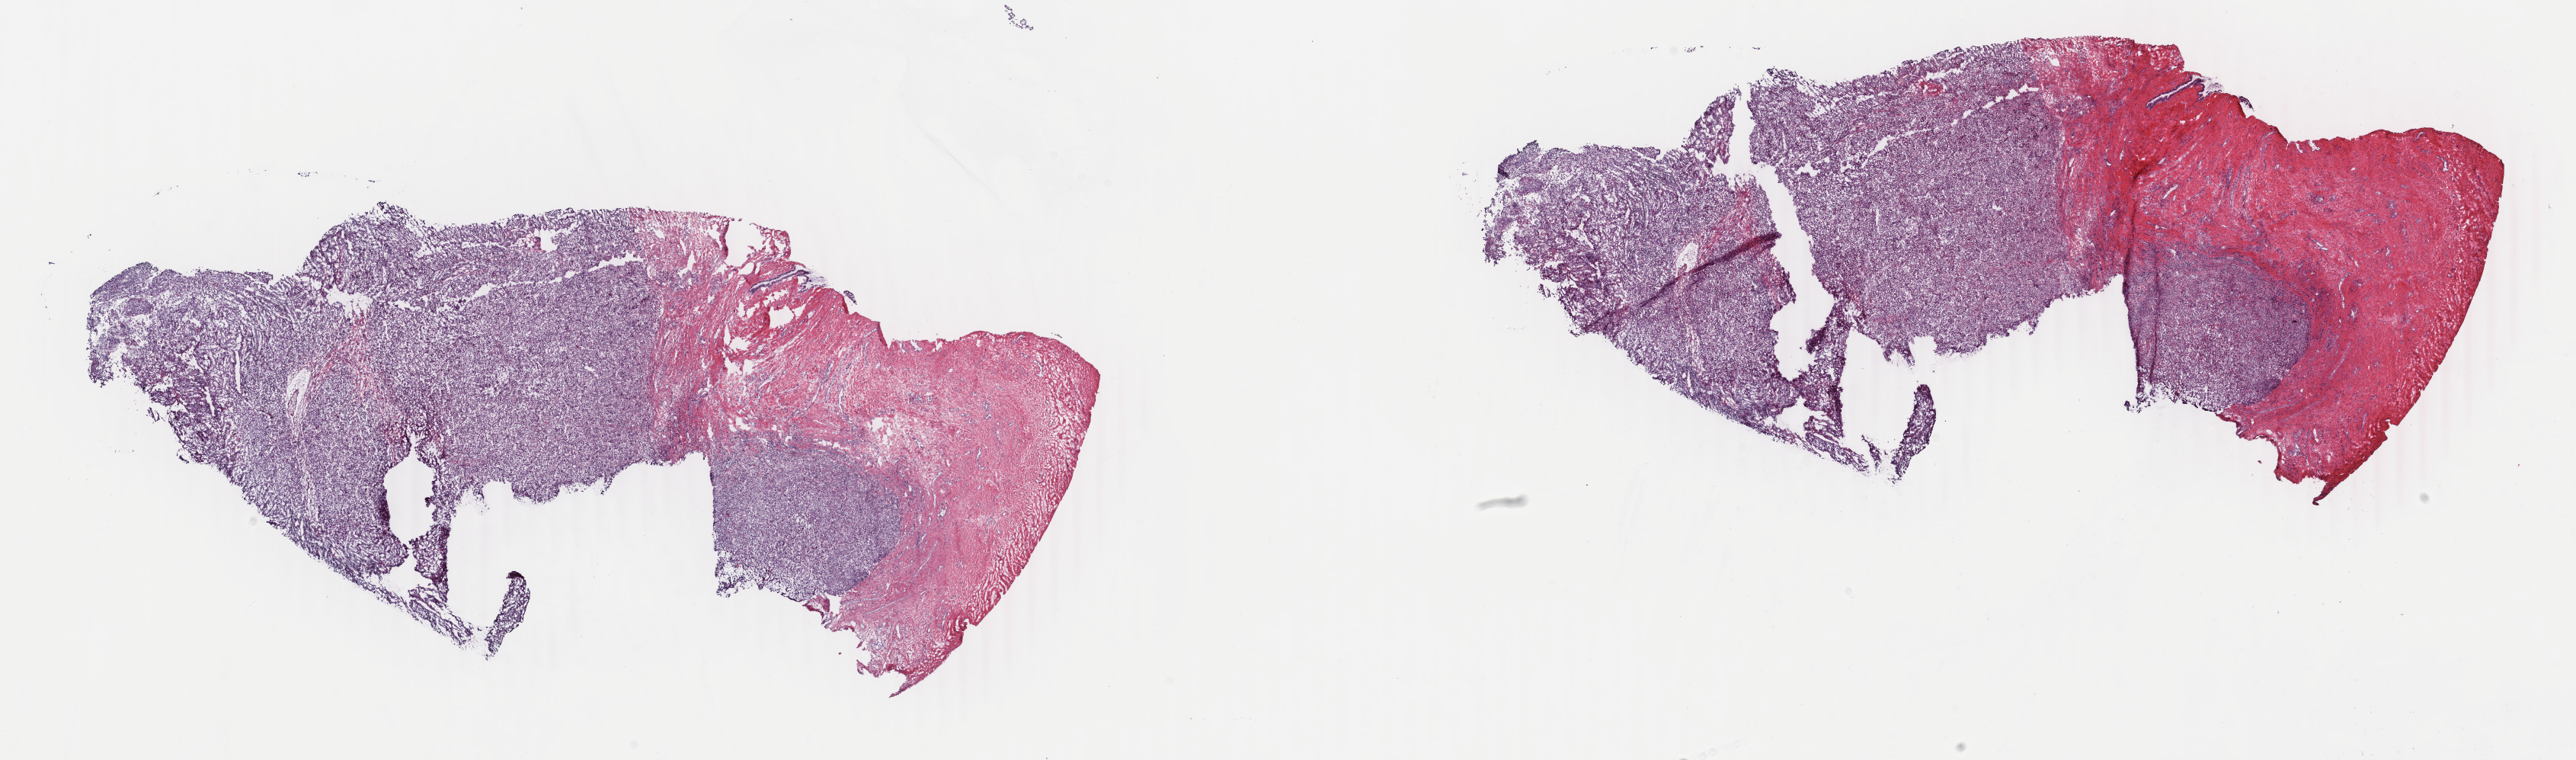
Whole-slide histology image, H&E — whole scanned area (about 26.9 x 7.9 mm, from a 40x scan) shown as a low-resolution overview, frozen section from the top of the tissue portion, cervix, primary tumour sample. Female patient; age at initial diagnosis 42 years. Histologic grade: G3 (poorly differentiated). Slide review estimates, as recorded: tumour cells 60%, tumour nuclei 60%, normal cells 0%, stromal cells 30%, necrosis 10%. Infiltration values recorded for this section: lymphocyte infiltration 40%, monocyte infiltration 20%, neutrophil infiltration 20%.
FIGO stage: IB. Diagnosis: Squamous cell carcinoma, large cell, nonkeratinizing, NOS (cervix uteri).